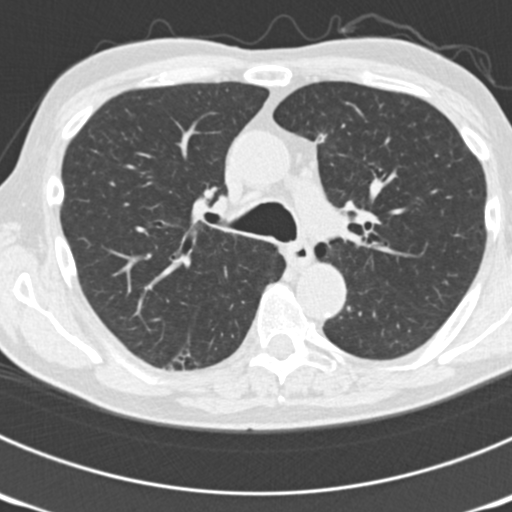
Low-dose screening chest CT, one axial slice. Slice 122 of 177 in the series (ordered by position). Reconstruction kernel B30f. 120 kVp. Lung window (W 1500 / L -600 HU). 512 × 512 image matrix.
Annotated regions visible in this slice (expert manual segmentation):
- lesion 4 (tumor): box from (x=315, y=132) to (x=329, y=145) px